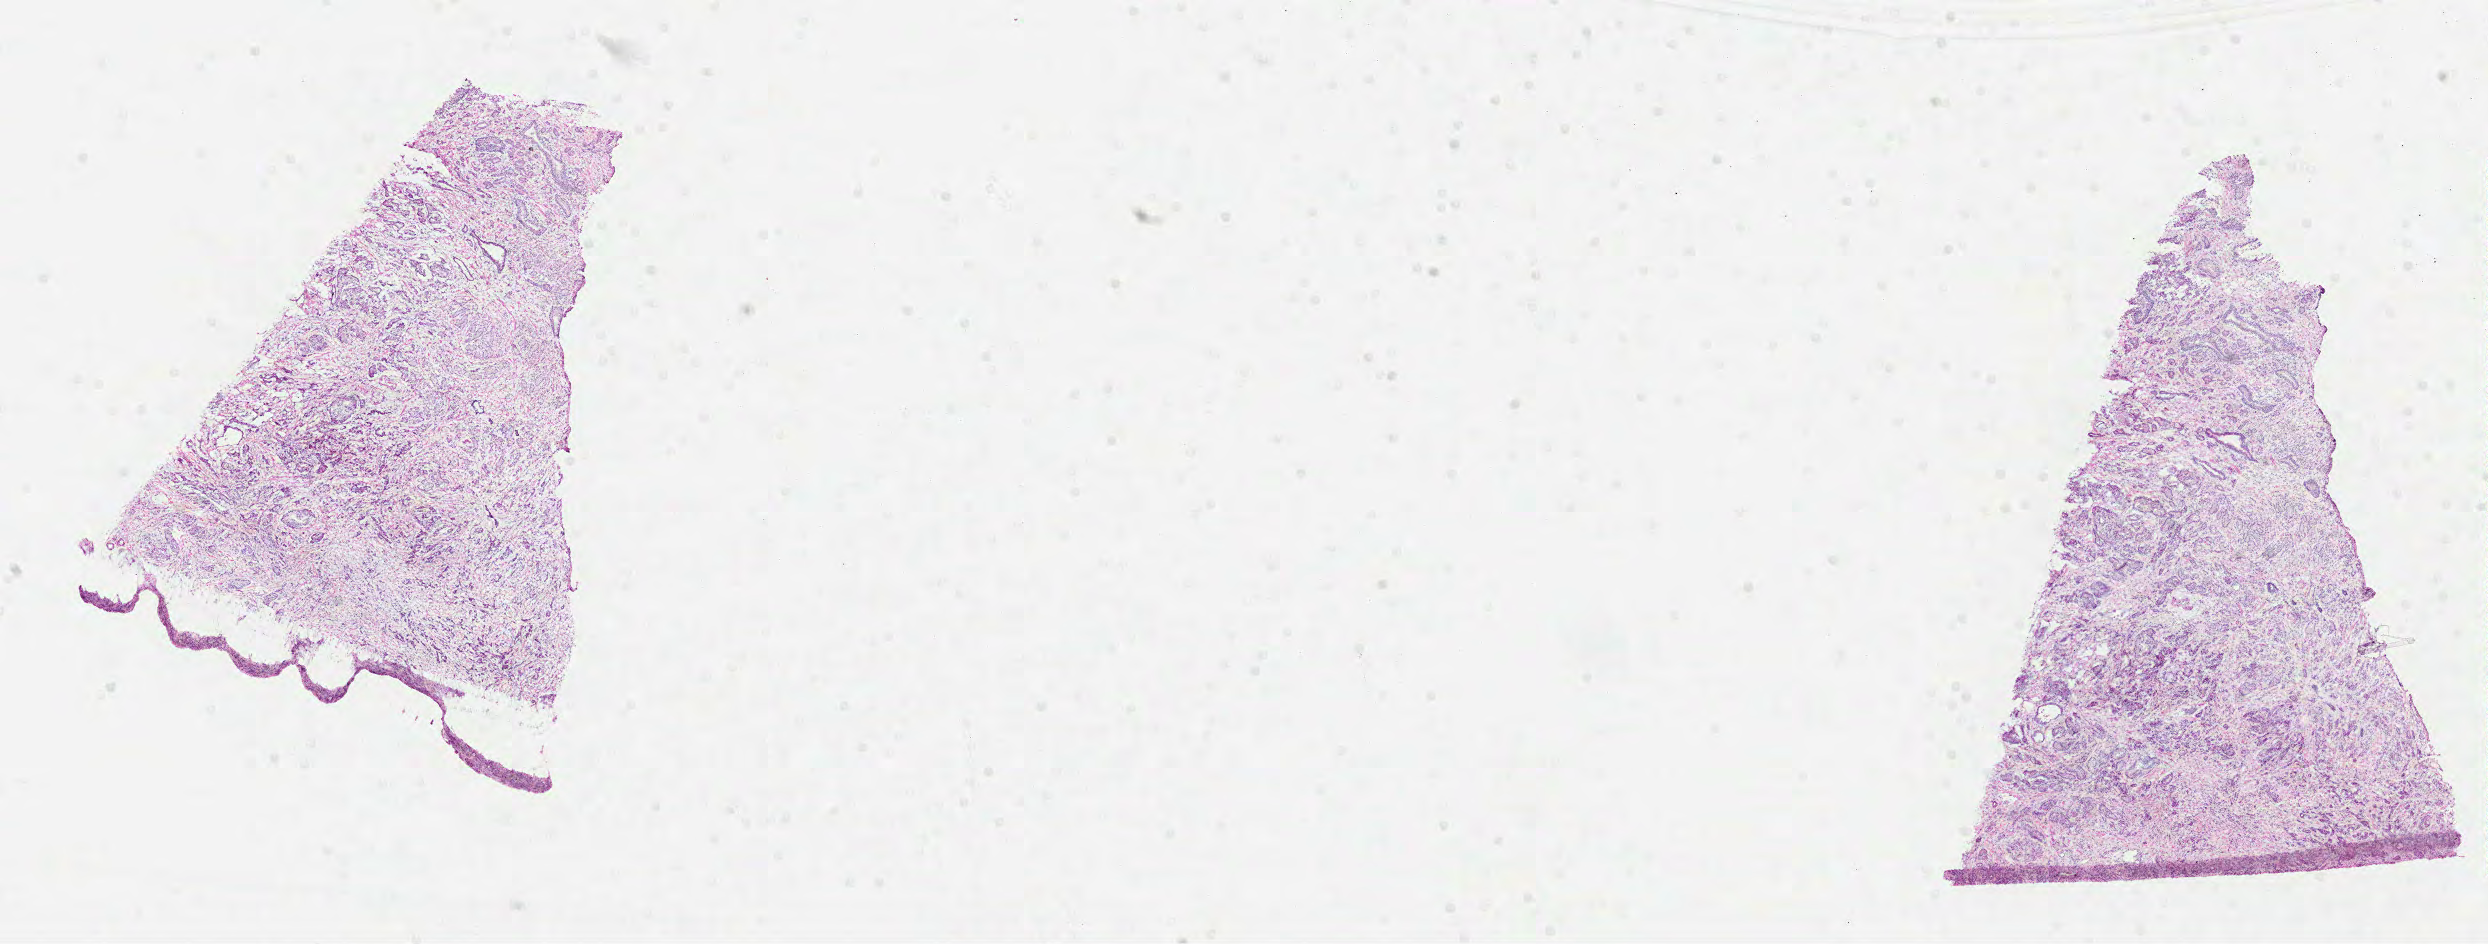
Digitized H&E-stained tissue section (whole slide), low-resolution overview of the scanned area, about 20.1 x 7.6 mm (slide scanned at 40x), FFPE section, prostate, primary tumour sample. Male, age 65 years at initial diagnosis. Gleason score: 7 (3+4).
Lymph nodes positive (case pathology): 0 of 8 examined. Diagnosis: Acinar cell carcinoma (prostate gland). Laterality: left.